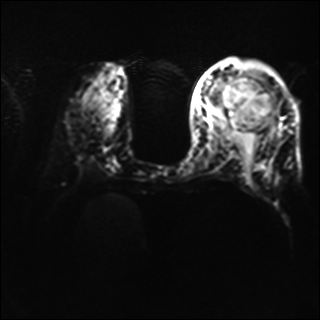
Breast MRI, one axial slice; diffusion-weighted series; image 2 of 4 stored at this slice position (different b-values; order by instance number); 1.5 T; 4 mm slice thickness; 320 × 320 image matrix. Female patient.
Annotated regions visible in this slice (manually delineated by an expert):
- tumour on diffusion-weighted imaging: bounding box <227,80,244,98> (left, top, right, bottom; pixels)